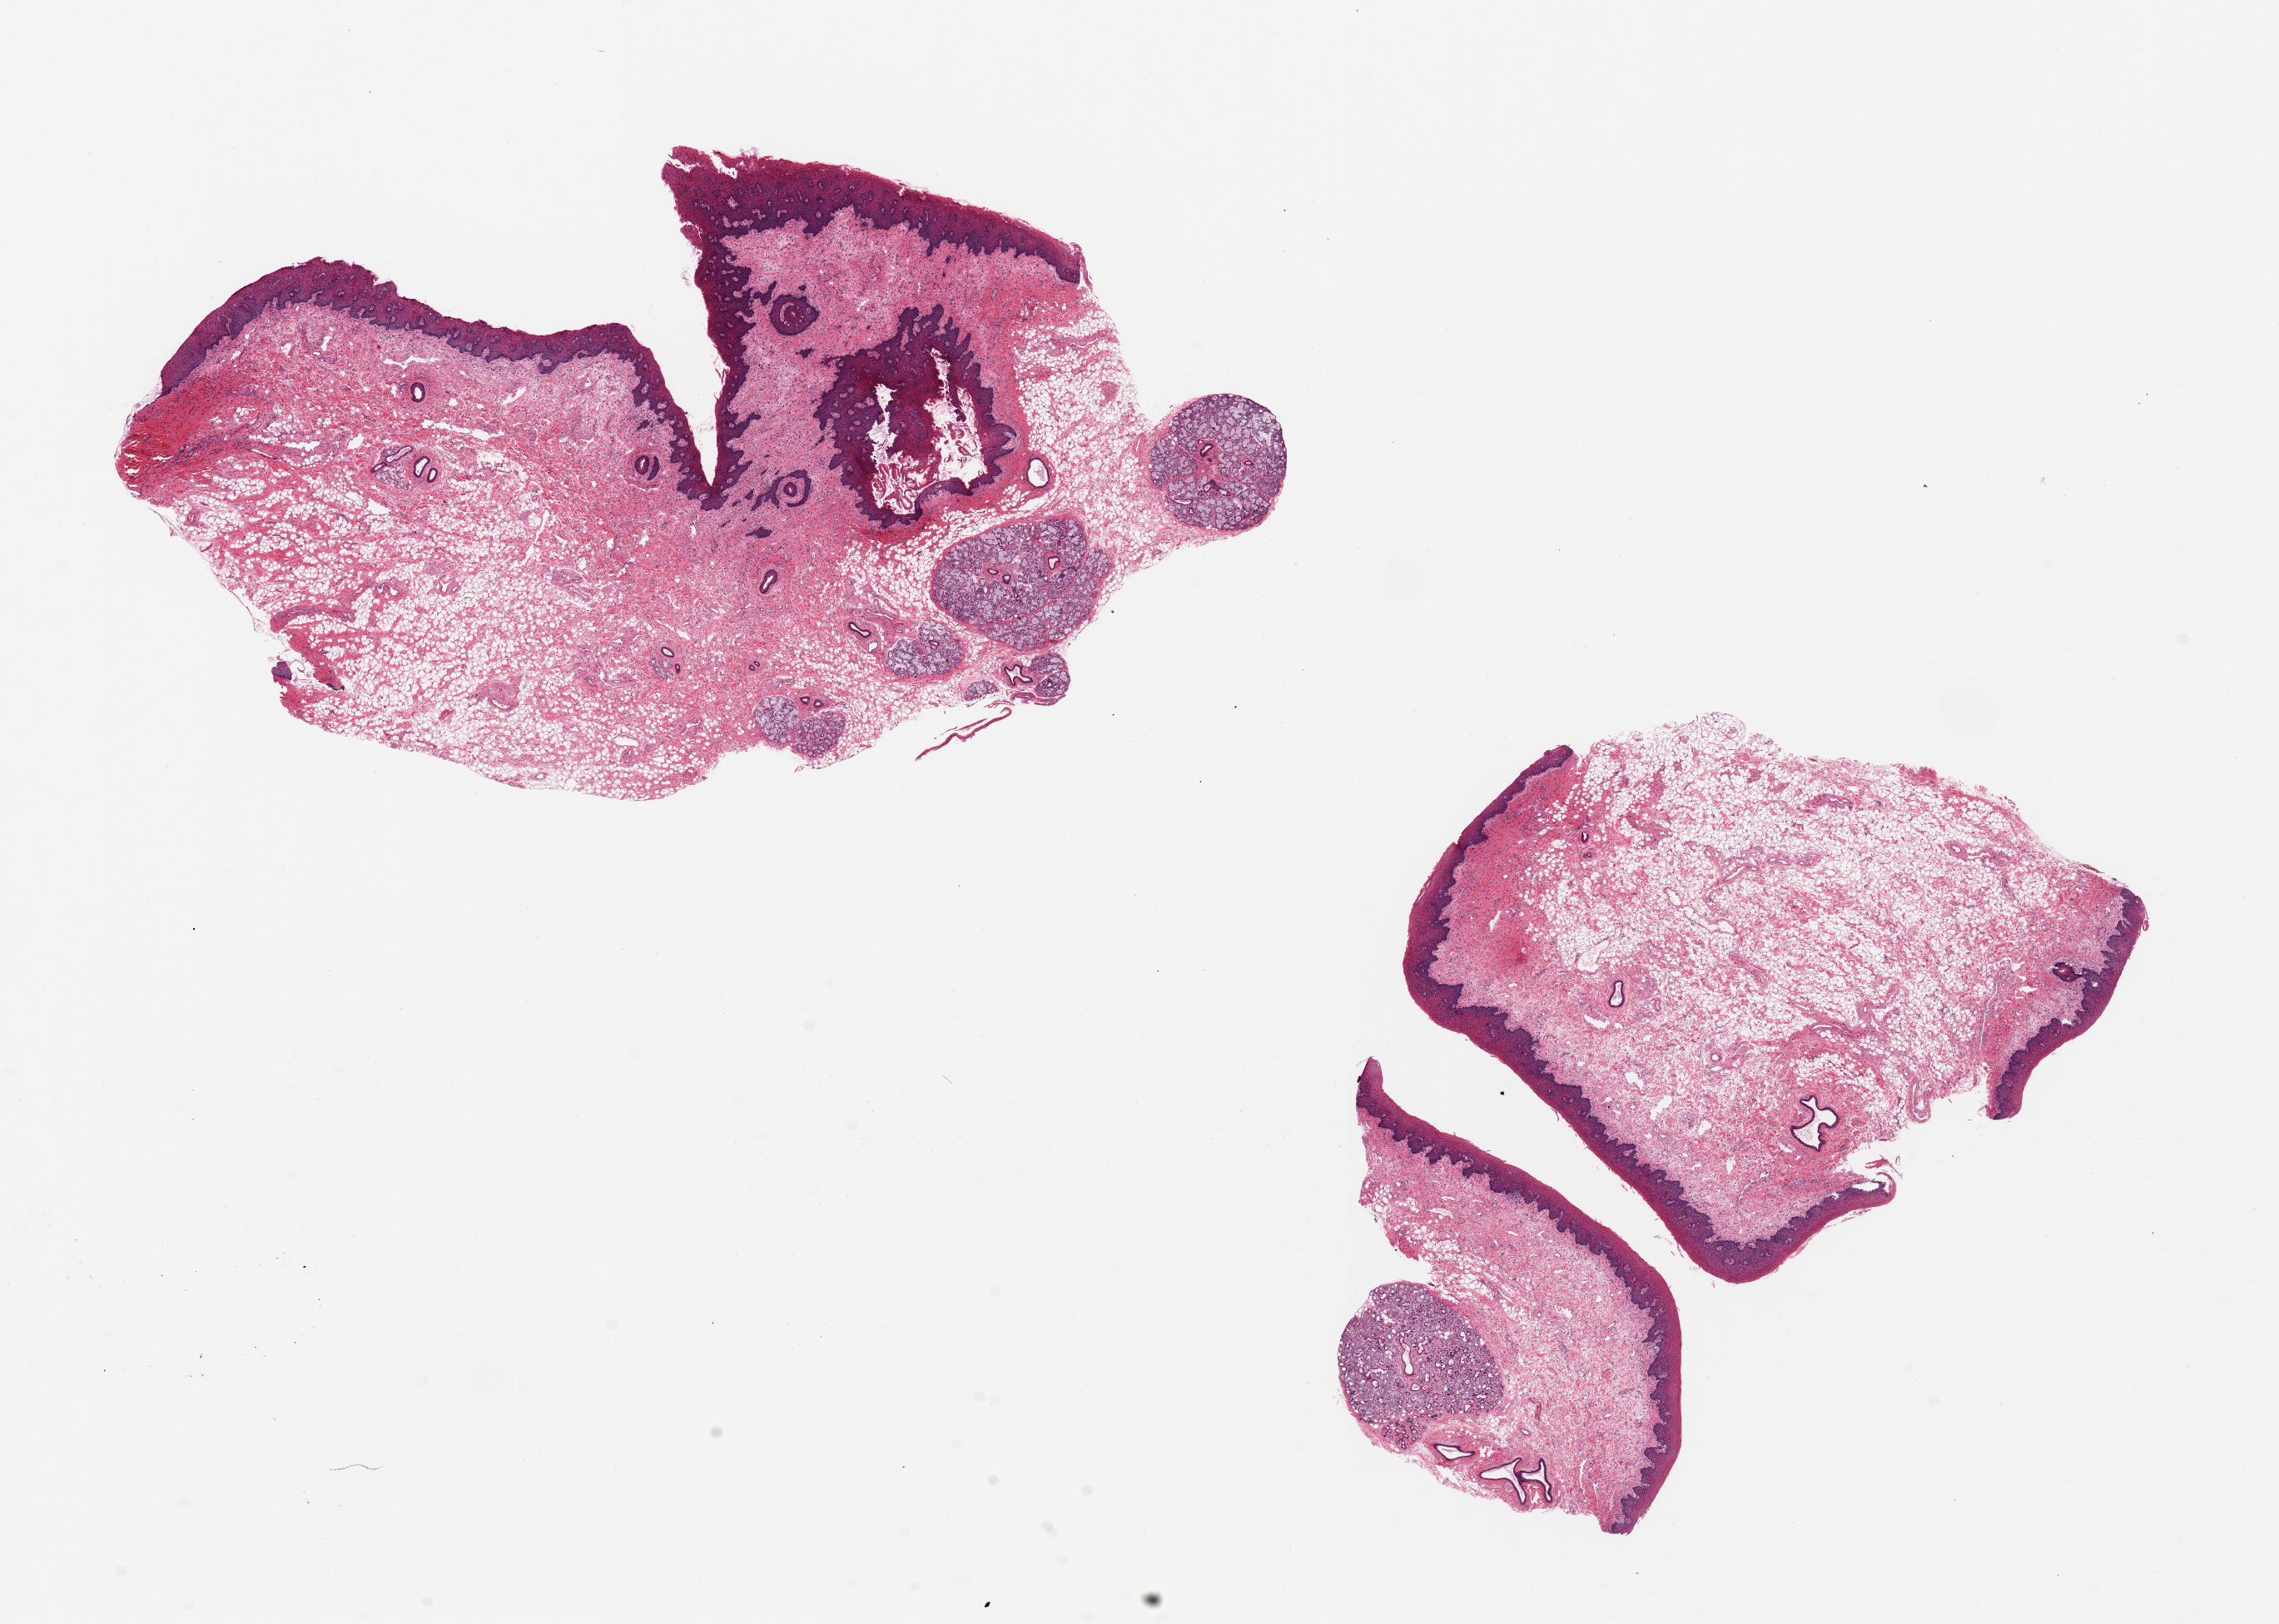
H&E whole-slide image, brightfield, whole scanned area (about 21.7 x 15.4 mm, from a 20x scan) shown as a low-resolution overview. PAXgene-fixed, paraffin-embedded tissue. Section of minor salivary gland (target tissue). Donor tissue sample. Donor sex: female.
Pathologist's review note for this sample: 3 pieces, up to 9x6mm; parakeratotic lip surface on all pieces; 4 glands in one piece, one gland in 1 piece, no gland in one piece with duct; glands are 0.7 to 1.5 mm across; 80% is lip epithelium and stroma.